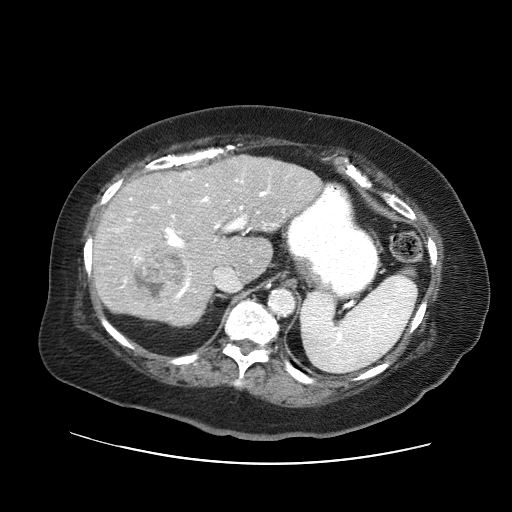
Contrast-enhanced abdominal CT (liver protocol), one axial slice; slice 36 of 71 in the series (ordered by position); reconstruction kernel STANDARD; 120 kVp; soft-tissue window (W 400 / L 40 HU); 2.5 mm slice thickness; 512 × 512 image matrix, field of view 400 × 400 mm. From the clinical record (not read from this slice): diagnosis: hepatocellular carcinoma (patient treated with transarterial chemoembolisation; whether this scan precedes or follows treatment is not stated here); TNM stage (as recorded): Stage-II; Child-Pugh class: A.
Structures marked on this image (semi-automatic segmentation, software-assisted and operator-edited):
- liver parenchyma outside the tumour (the mass and vessels are separate outlines, so this box may not span the whole liver): bounding box (x1, y1, x2, y2) in pixels: (92, 154, 322, 324)
- mass: (135, 244, 187, 298)
- liver vessels: (108, 172, 284, 299)